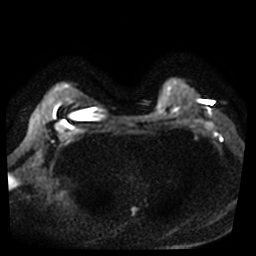
Breast MRI, one axial slice; position 33 of 40 along the scan axis; diffusion-weighted series; image 2 of 4 stored at this slice position (different b-values; order by instance number); 3 T; 5 mm slice thickness; 256 × 256 image matrix. Female patient.
Annotated regions visible in this slice (outlined manually by an expert reader):
- tumour on diffusion-weighted imaging: bounding box (x1, y1, x2, y2) in pixels: (208, 110, 211, 114)